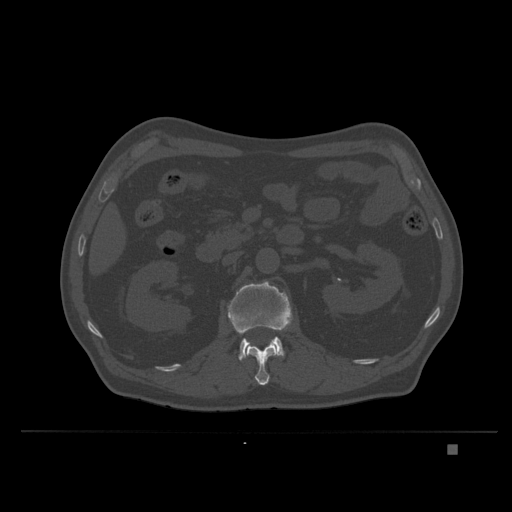
CT including the spine, one axial slice. Position 127 of 435 along the scan axis. Bone window (W 1800 / L 400 HU). 1.5 mm slice thickness. 512 × 512 image matrix, field of view 434 × 434 mm. Male patient, age 73 years. Case-level facts recorded for this patient, not image findings: primary cancer: skin.
Structures marked on this image (semi-automatically segmented with operator editing):
- L1 vertebra: box from (x=244, y=340) to (x=278, y=385) px
- L2 vertebra: (x=227, y=280)–(x=294, y=360)